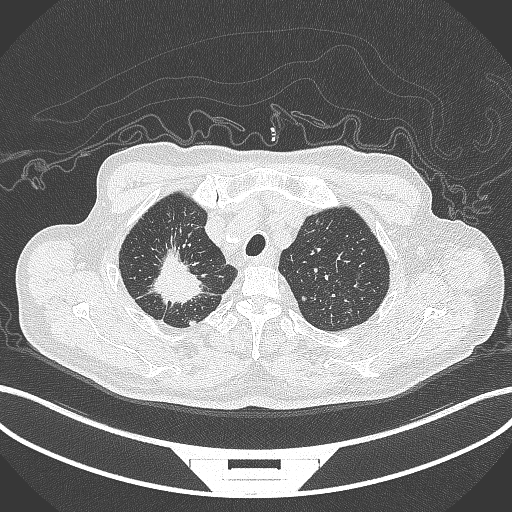
Chest CT, one axial slice; slice 326 of 407 in the series (ordered by position); reconstruction kernel B70f; 120 kVp; lung window (W 1500 / L -600 HU); 1 mm slice thickness; 512 × 512 image matrix, field of view 400 × 400 mm. Male patient, age 69 years. From the clinical record (not read from this slice): clinical TNM (as recorded): T1c N1 M1.
Outlined on this slice (bounding box drawn by a radiologist):
- lung tumour (recorded histology: adenocarcinoma): box from (x=137, y=241) to (x=208, y=307) px